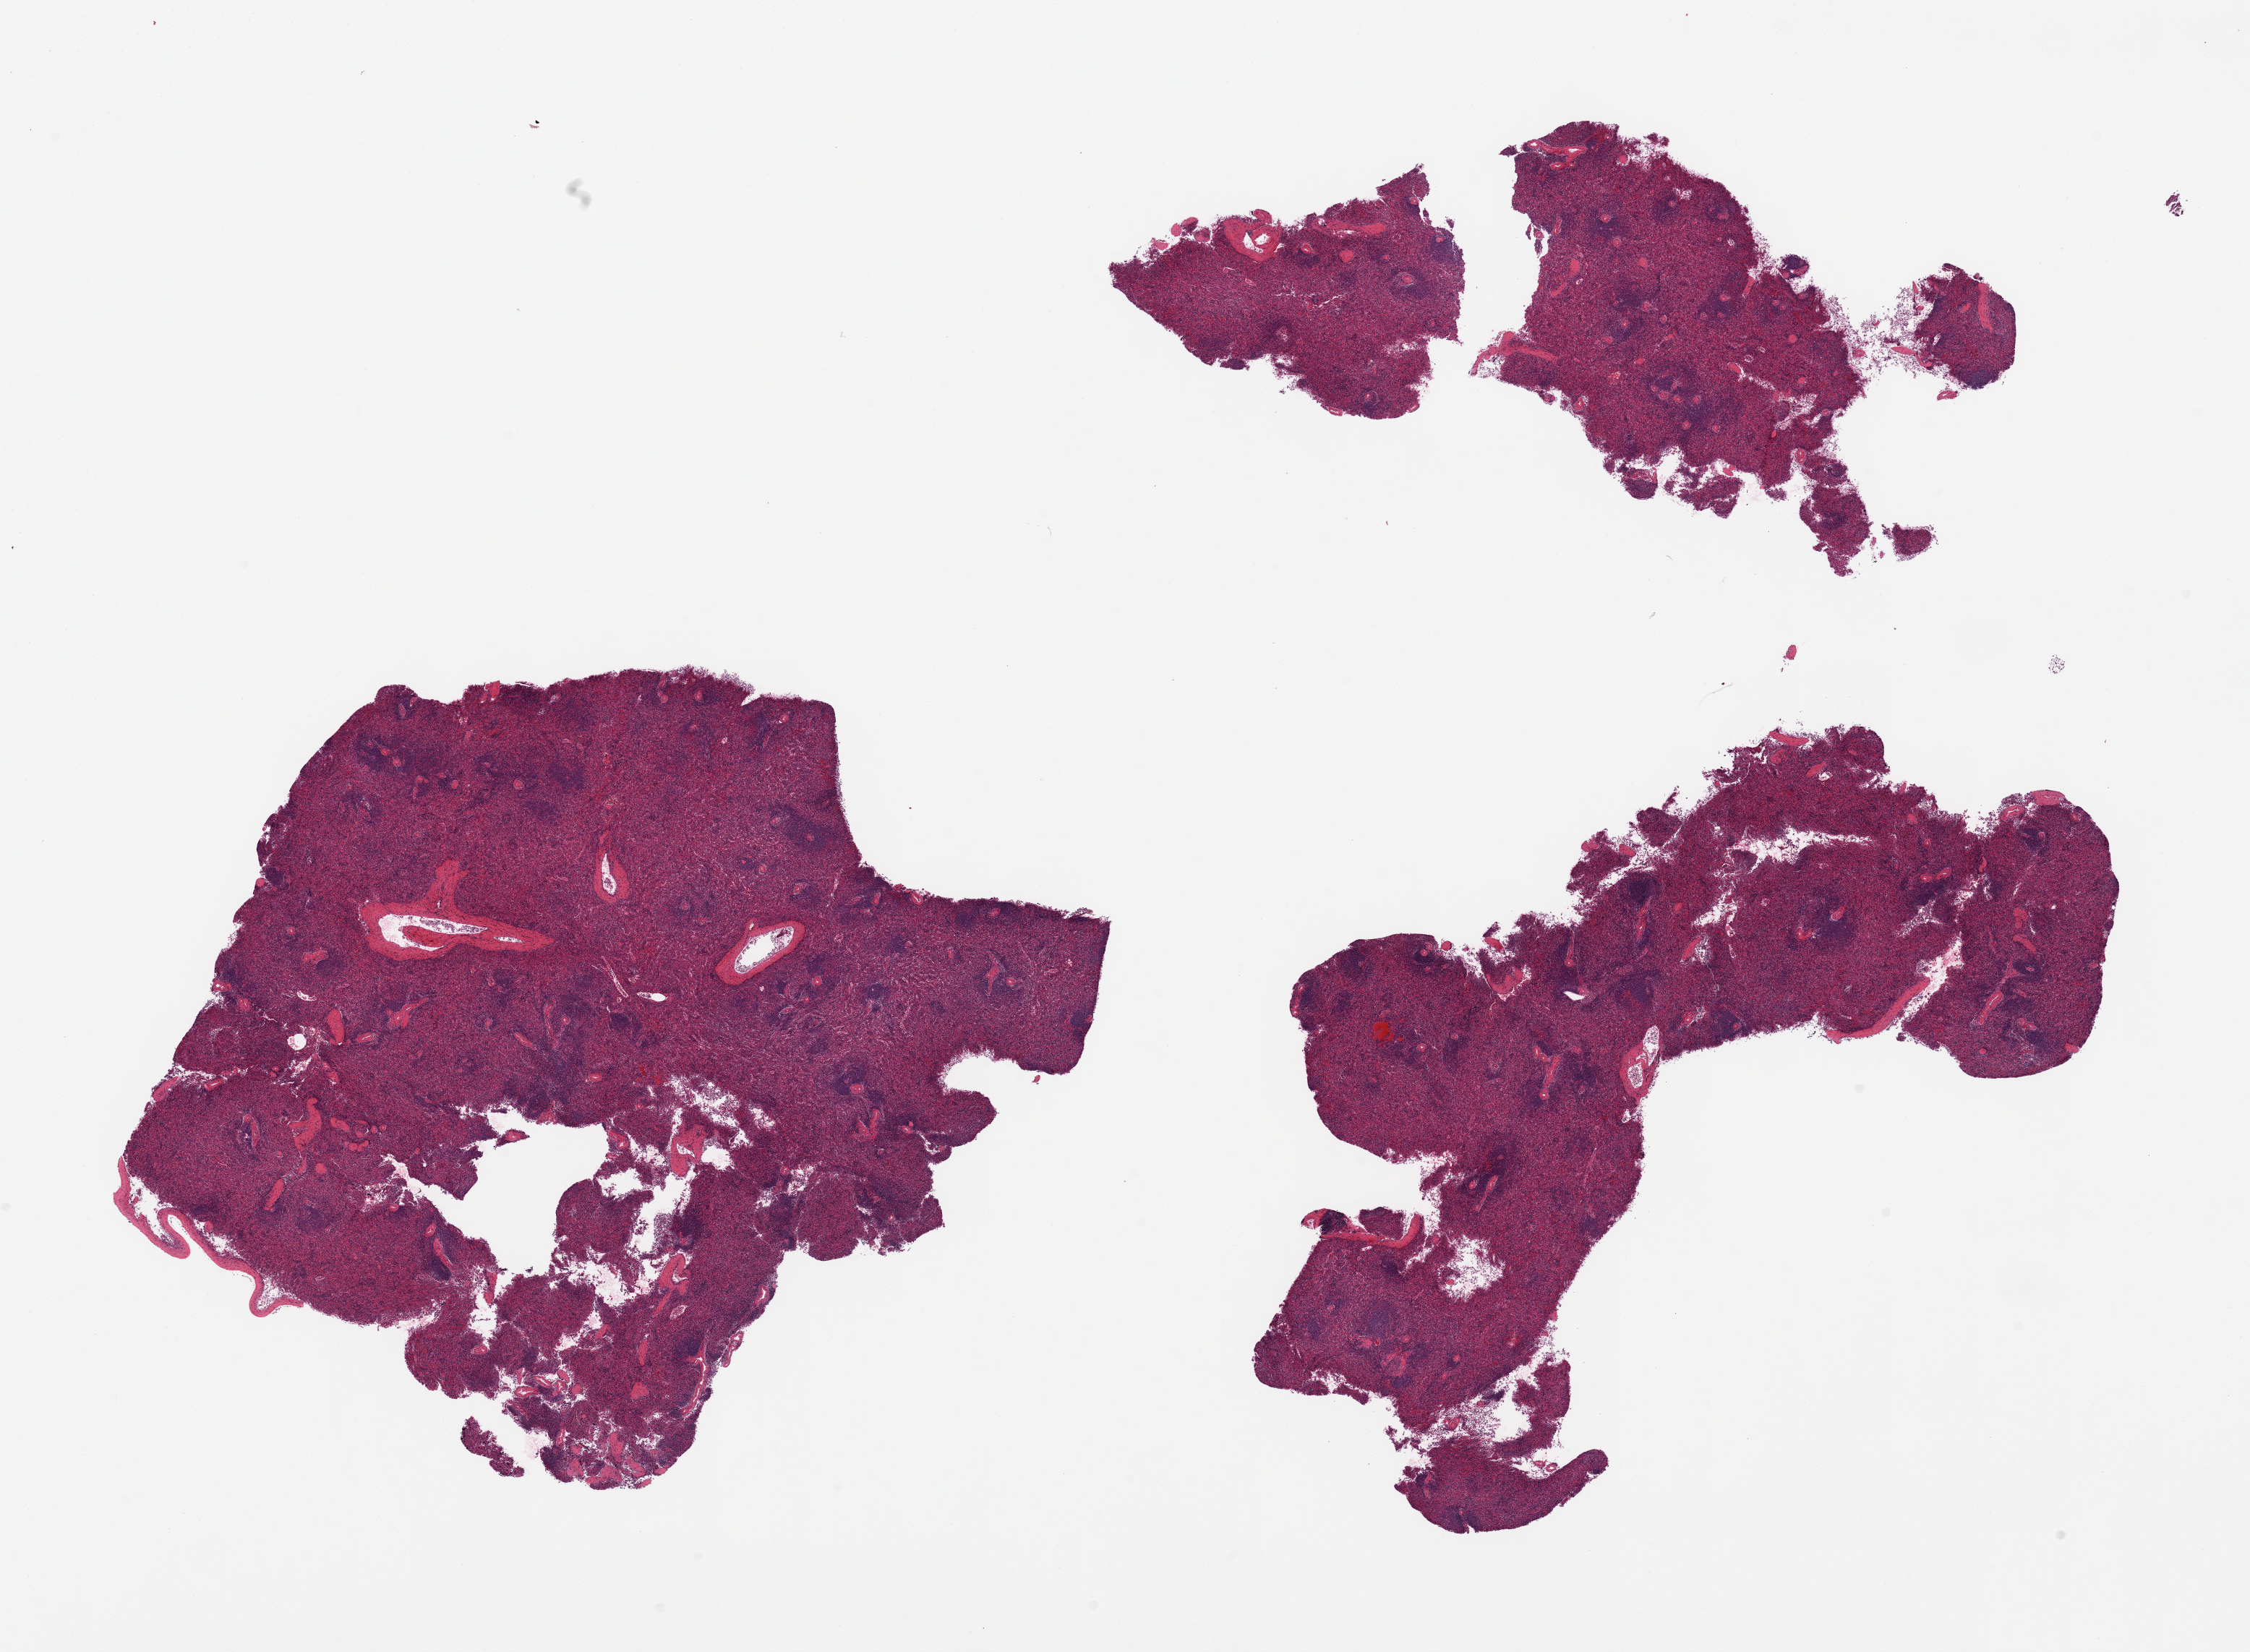
Digitized H&E-stained section, a low-resolution overview of the entire scanned area, about 24.6 x 18.1 mm (acquisition: 20x scan), PAXgene-fixed, paraffin-embedded tissue, section of spleen (target tissue), donor tissue sample. Donor sex: female.
Pathologist's review note for this sample: 2 pieces, fairly well preserved; no significant abnormalities.